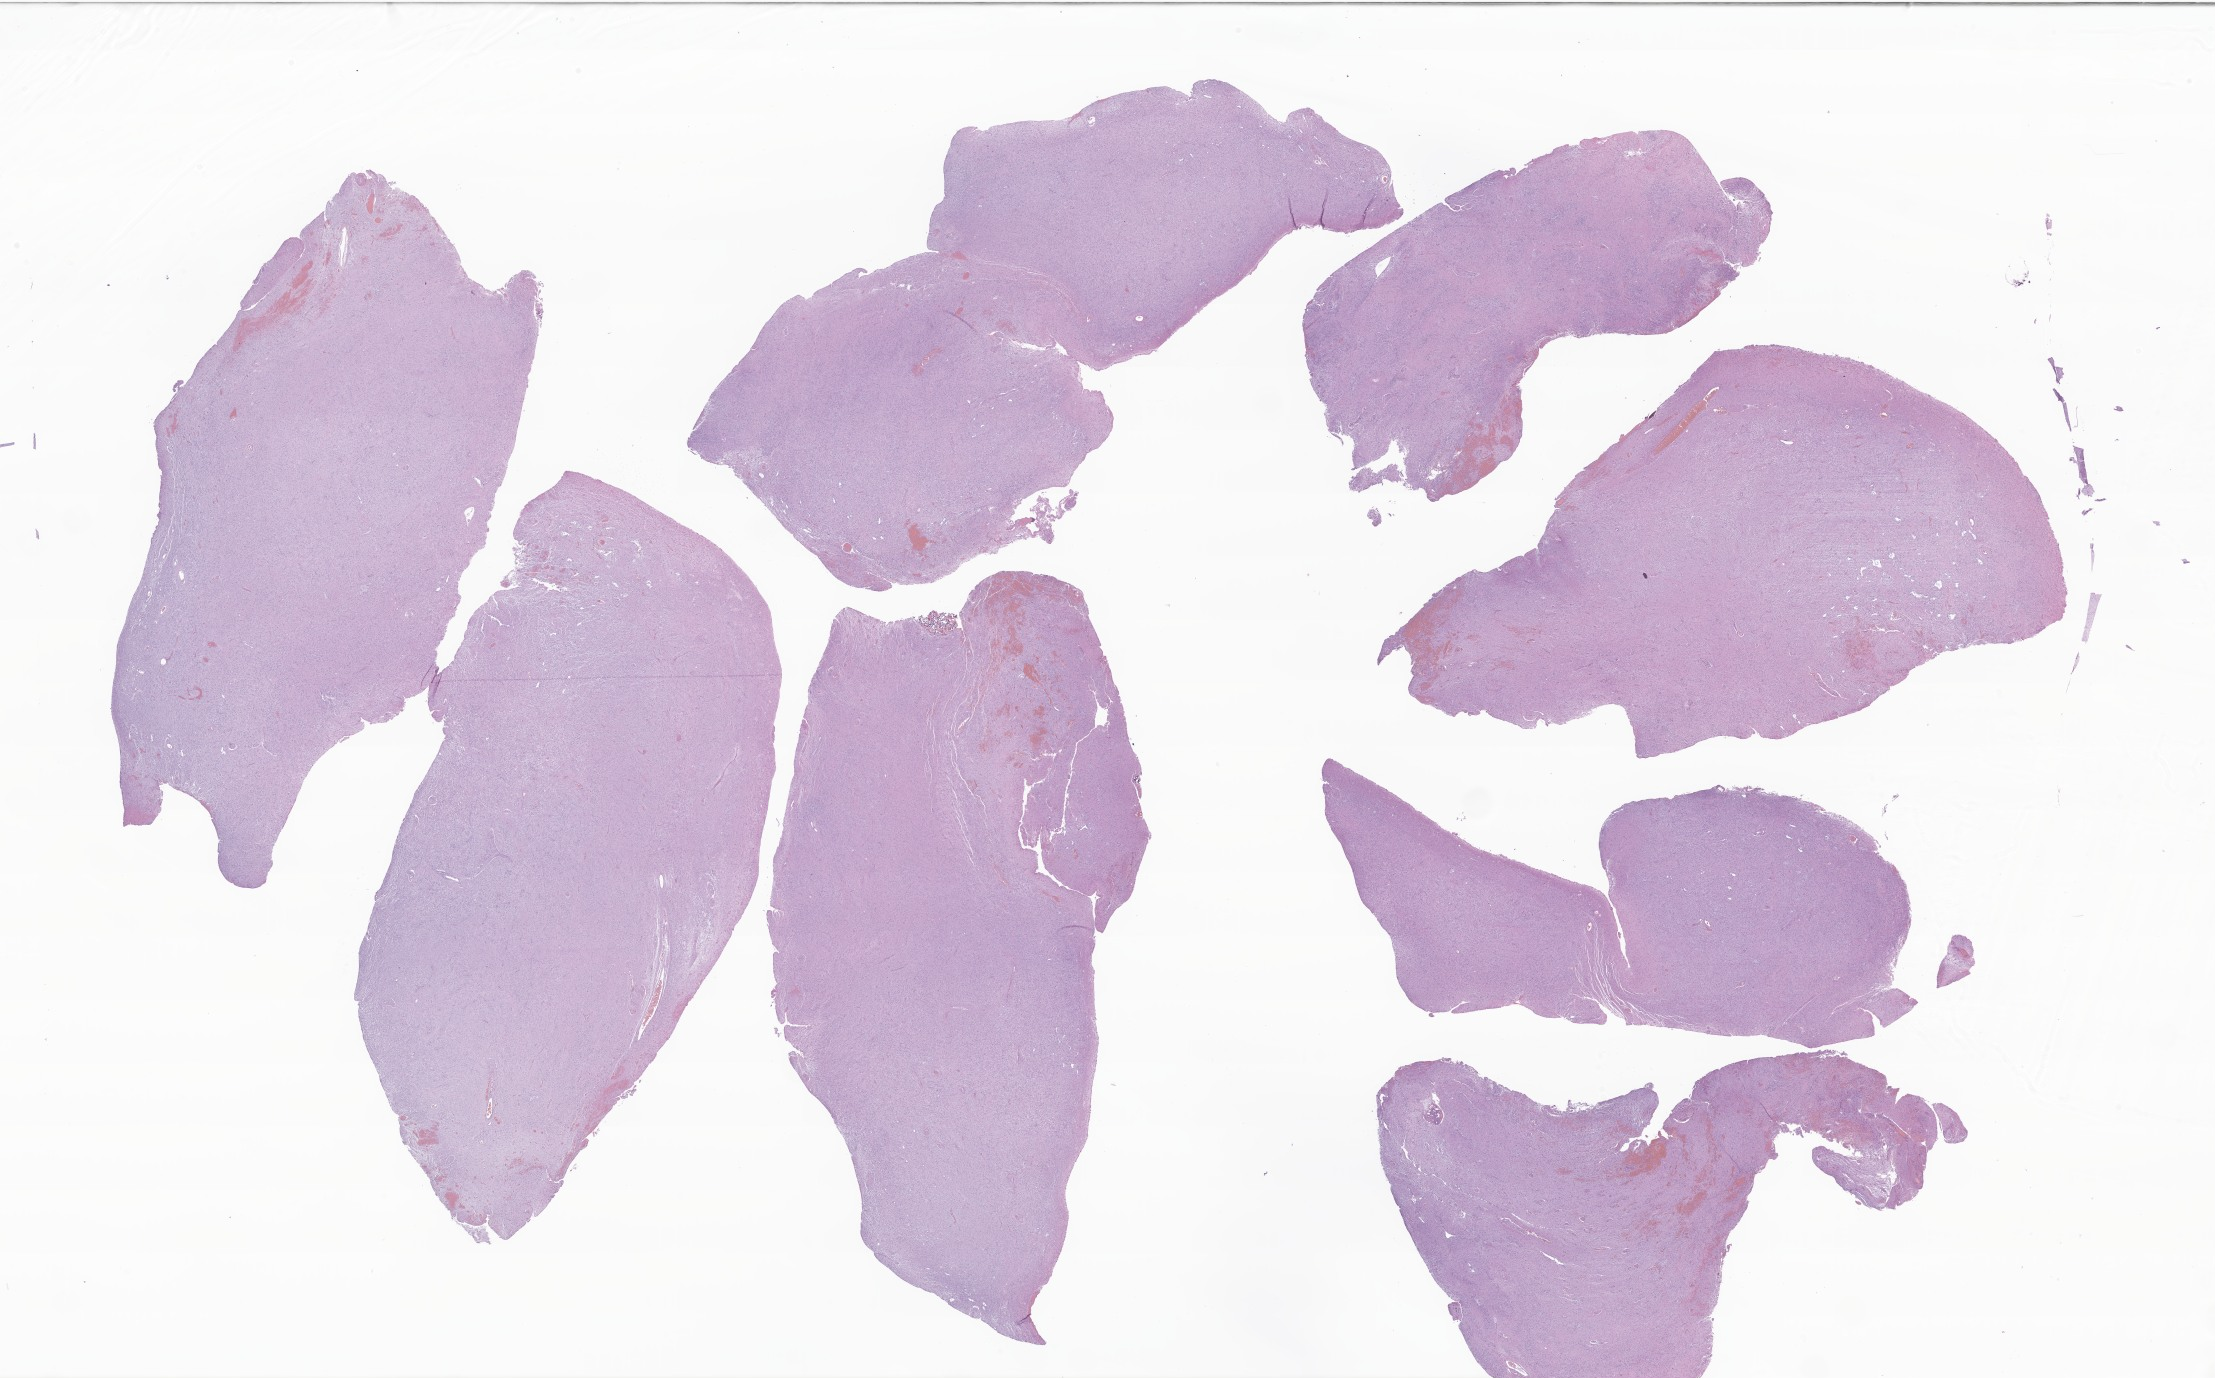
Whole-slide image, hematoxylin and eosin (H&E) stain of tumor tissue from the cerebellum — whole scanned area (about 37.4 x 23.2 mm) shown as a low-resolution overview; FFPE section. Patient: female, age 101 months (8 years 5 months).
* diagnosis (ICD-O-3 morphology term): Pilocytic astrocytoma